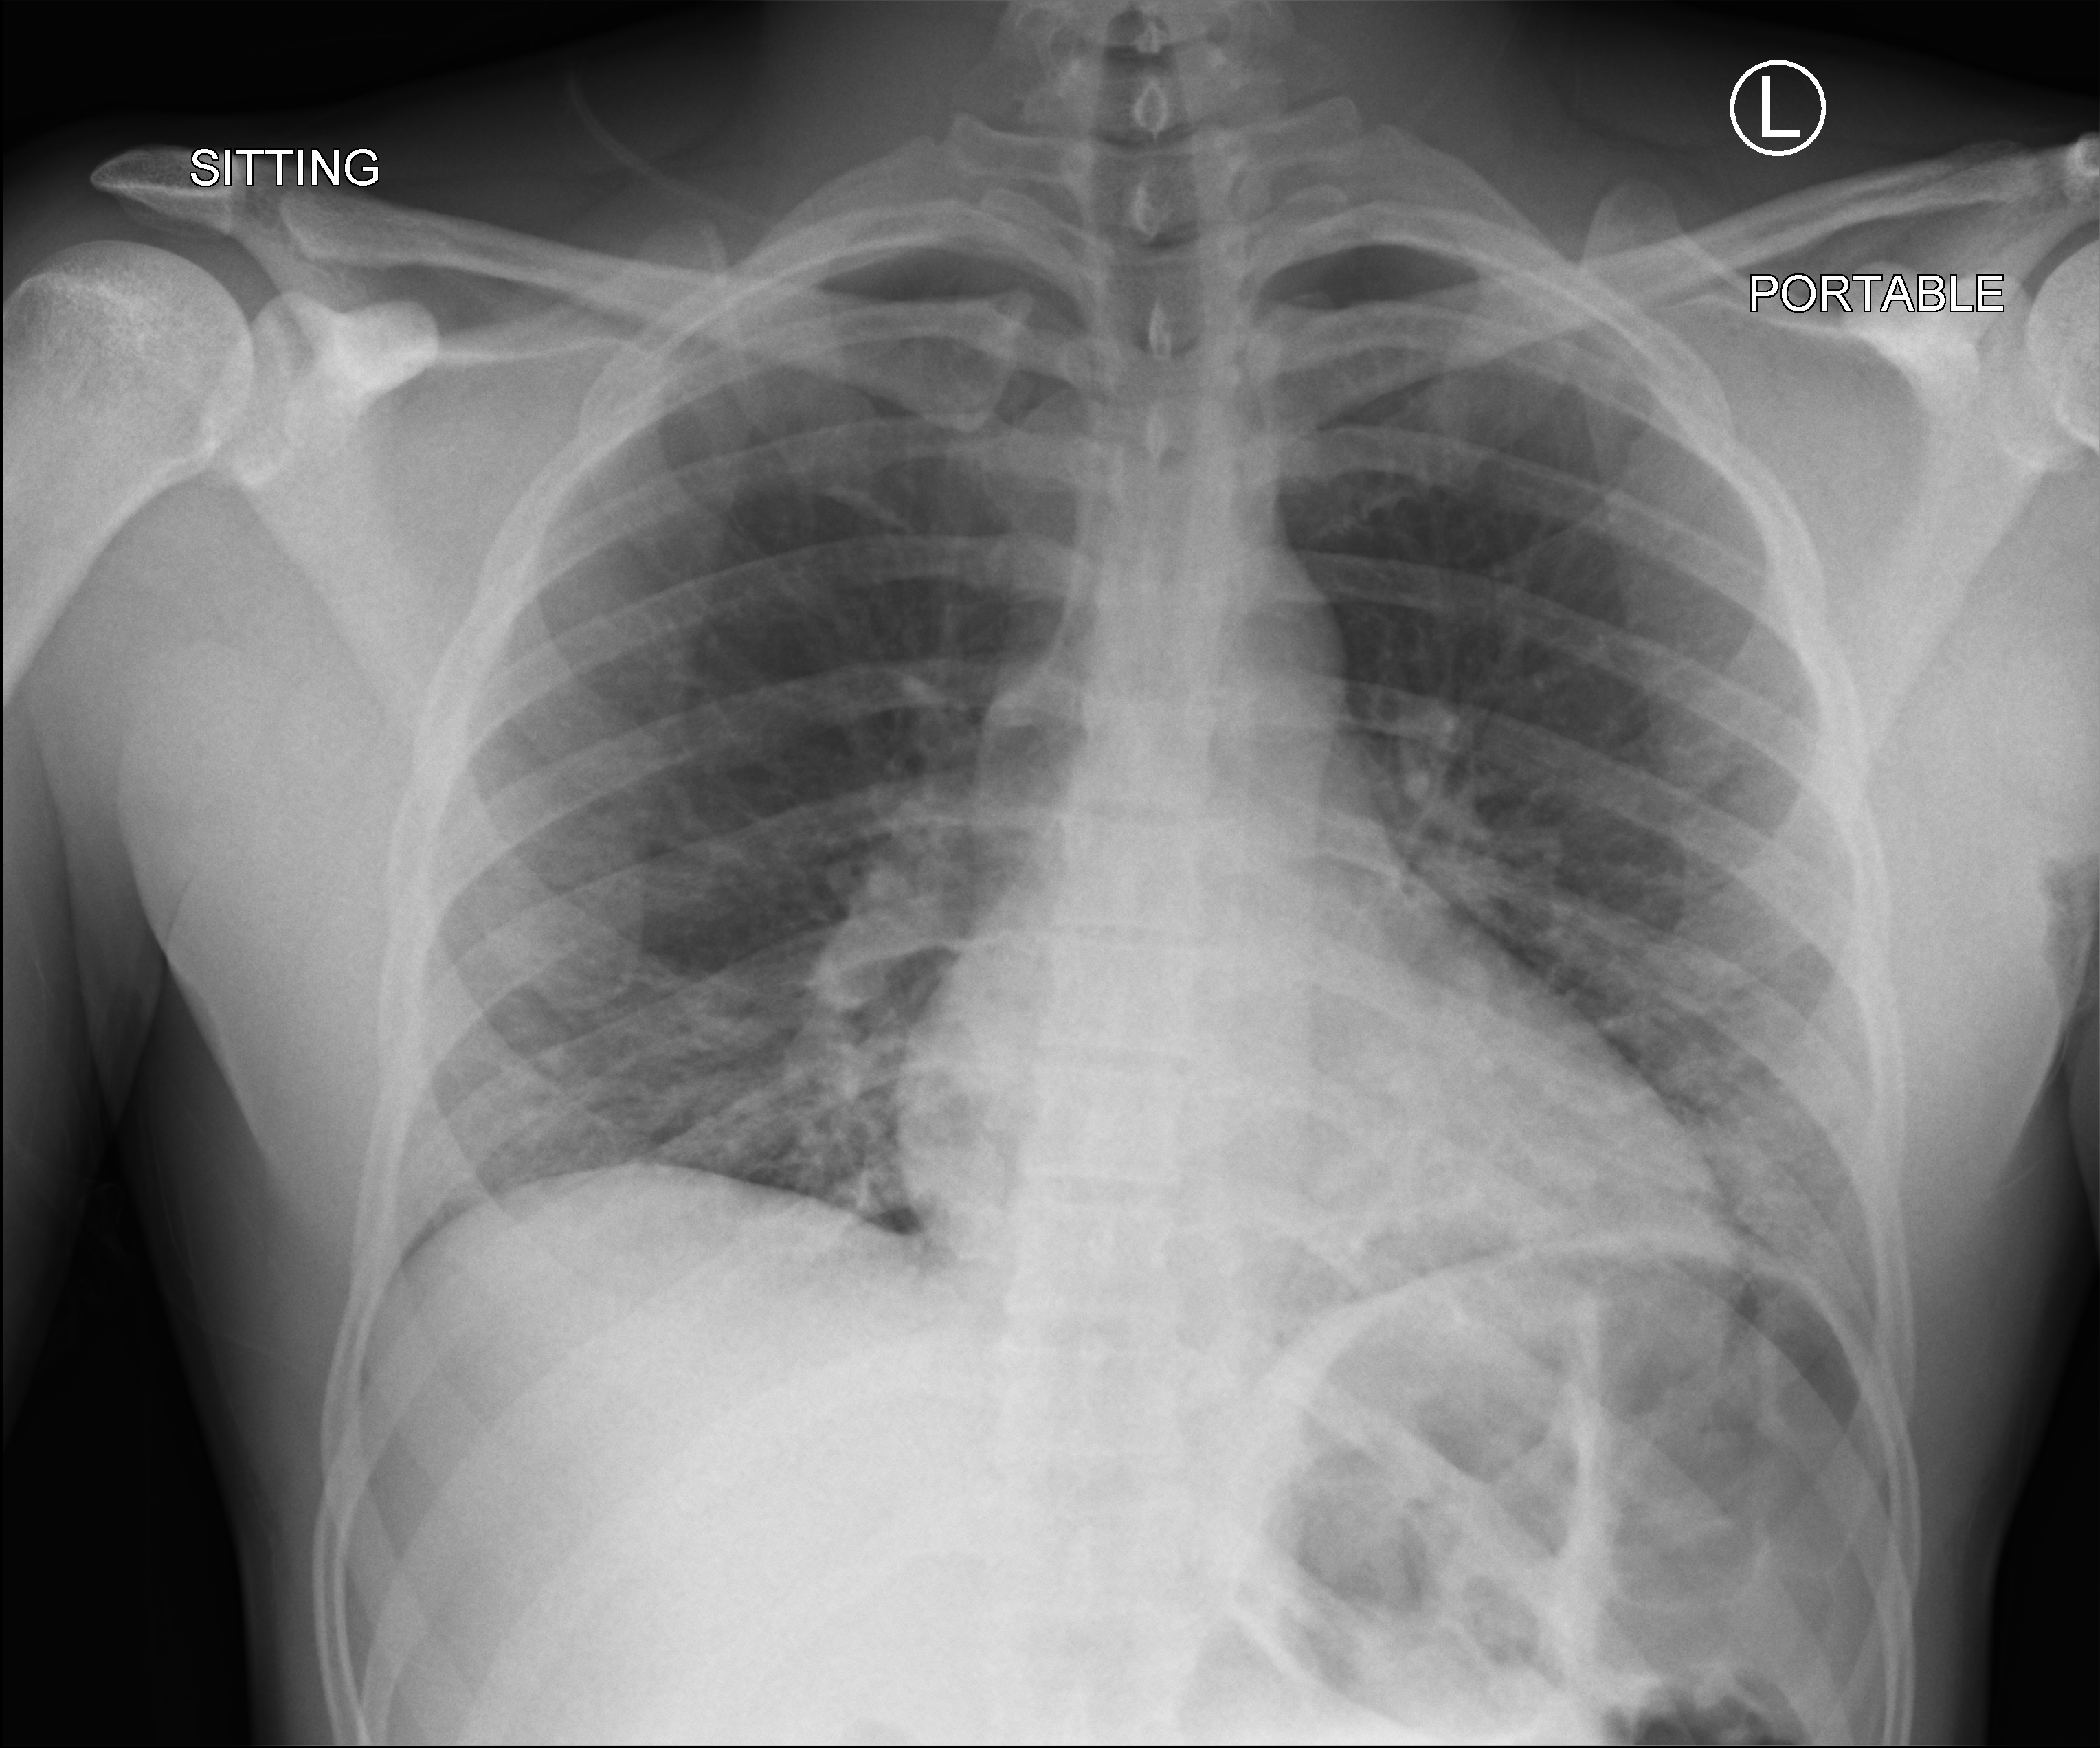
Portable chest radiograph; anteroposterior (AP) projection. Patient hospitalised with COVID-19; male, aged 18–59 years.
From the hospital-stay record, not from the radiograph (when in the stay this image was taken is not recorded): mechanically ventilated during this hospital stay: no.